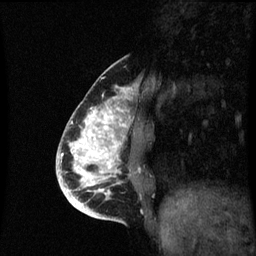
Breast MRI (dynamic contrast-enhanced), one sagittal slice. Slice 22 of 60 in the series (ordered by position). Dynamic contrast-enhanced series, image 2 of 3 at this slice position (ordered by acquisition). 1.5 T. TE 4.2 ms, TR 8.9 ms. 2 mm slice thickness. 256 × 256 image matrix, field of view 200 × 200 mm. Patient: female, 35 years. Case-level facts recorded for this patient, not image findings: setting: breast cancer imaged before/during neoadjuvant chemotherapy; receptor status: HR-positive, HER2-negative.
Structures marked on this image (semi-automatic segmentation, software-assisted and operator-edited):
- analysis volume of interest (the breast-tissue region the enhancement analysis was run in; not a lesion): bounding box (x1, y1, x2, y2) in pixels: (66, 100, 137, 215)
- tumour enhancement mask (voxels above the 70 % enhancement threshold inside the analysis volume of interest): (66, 106, 126, 215)